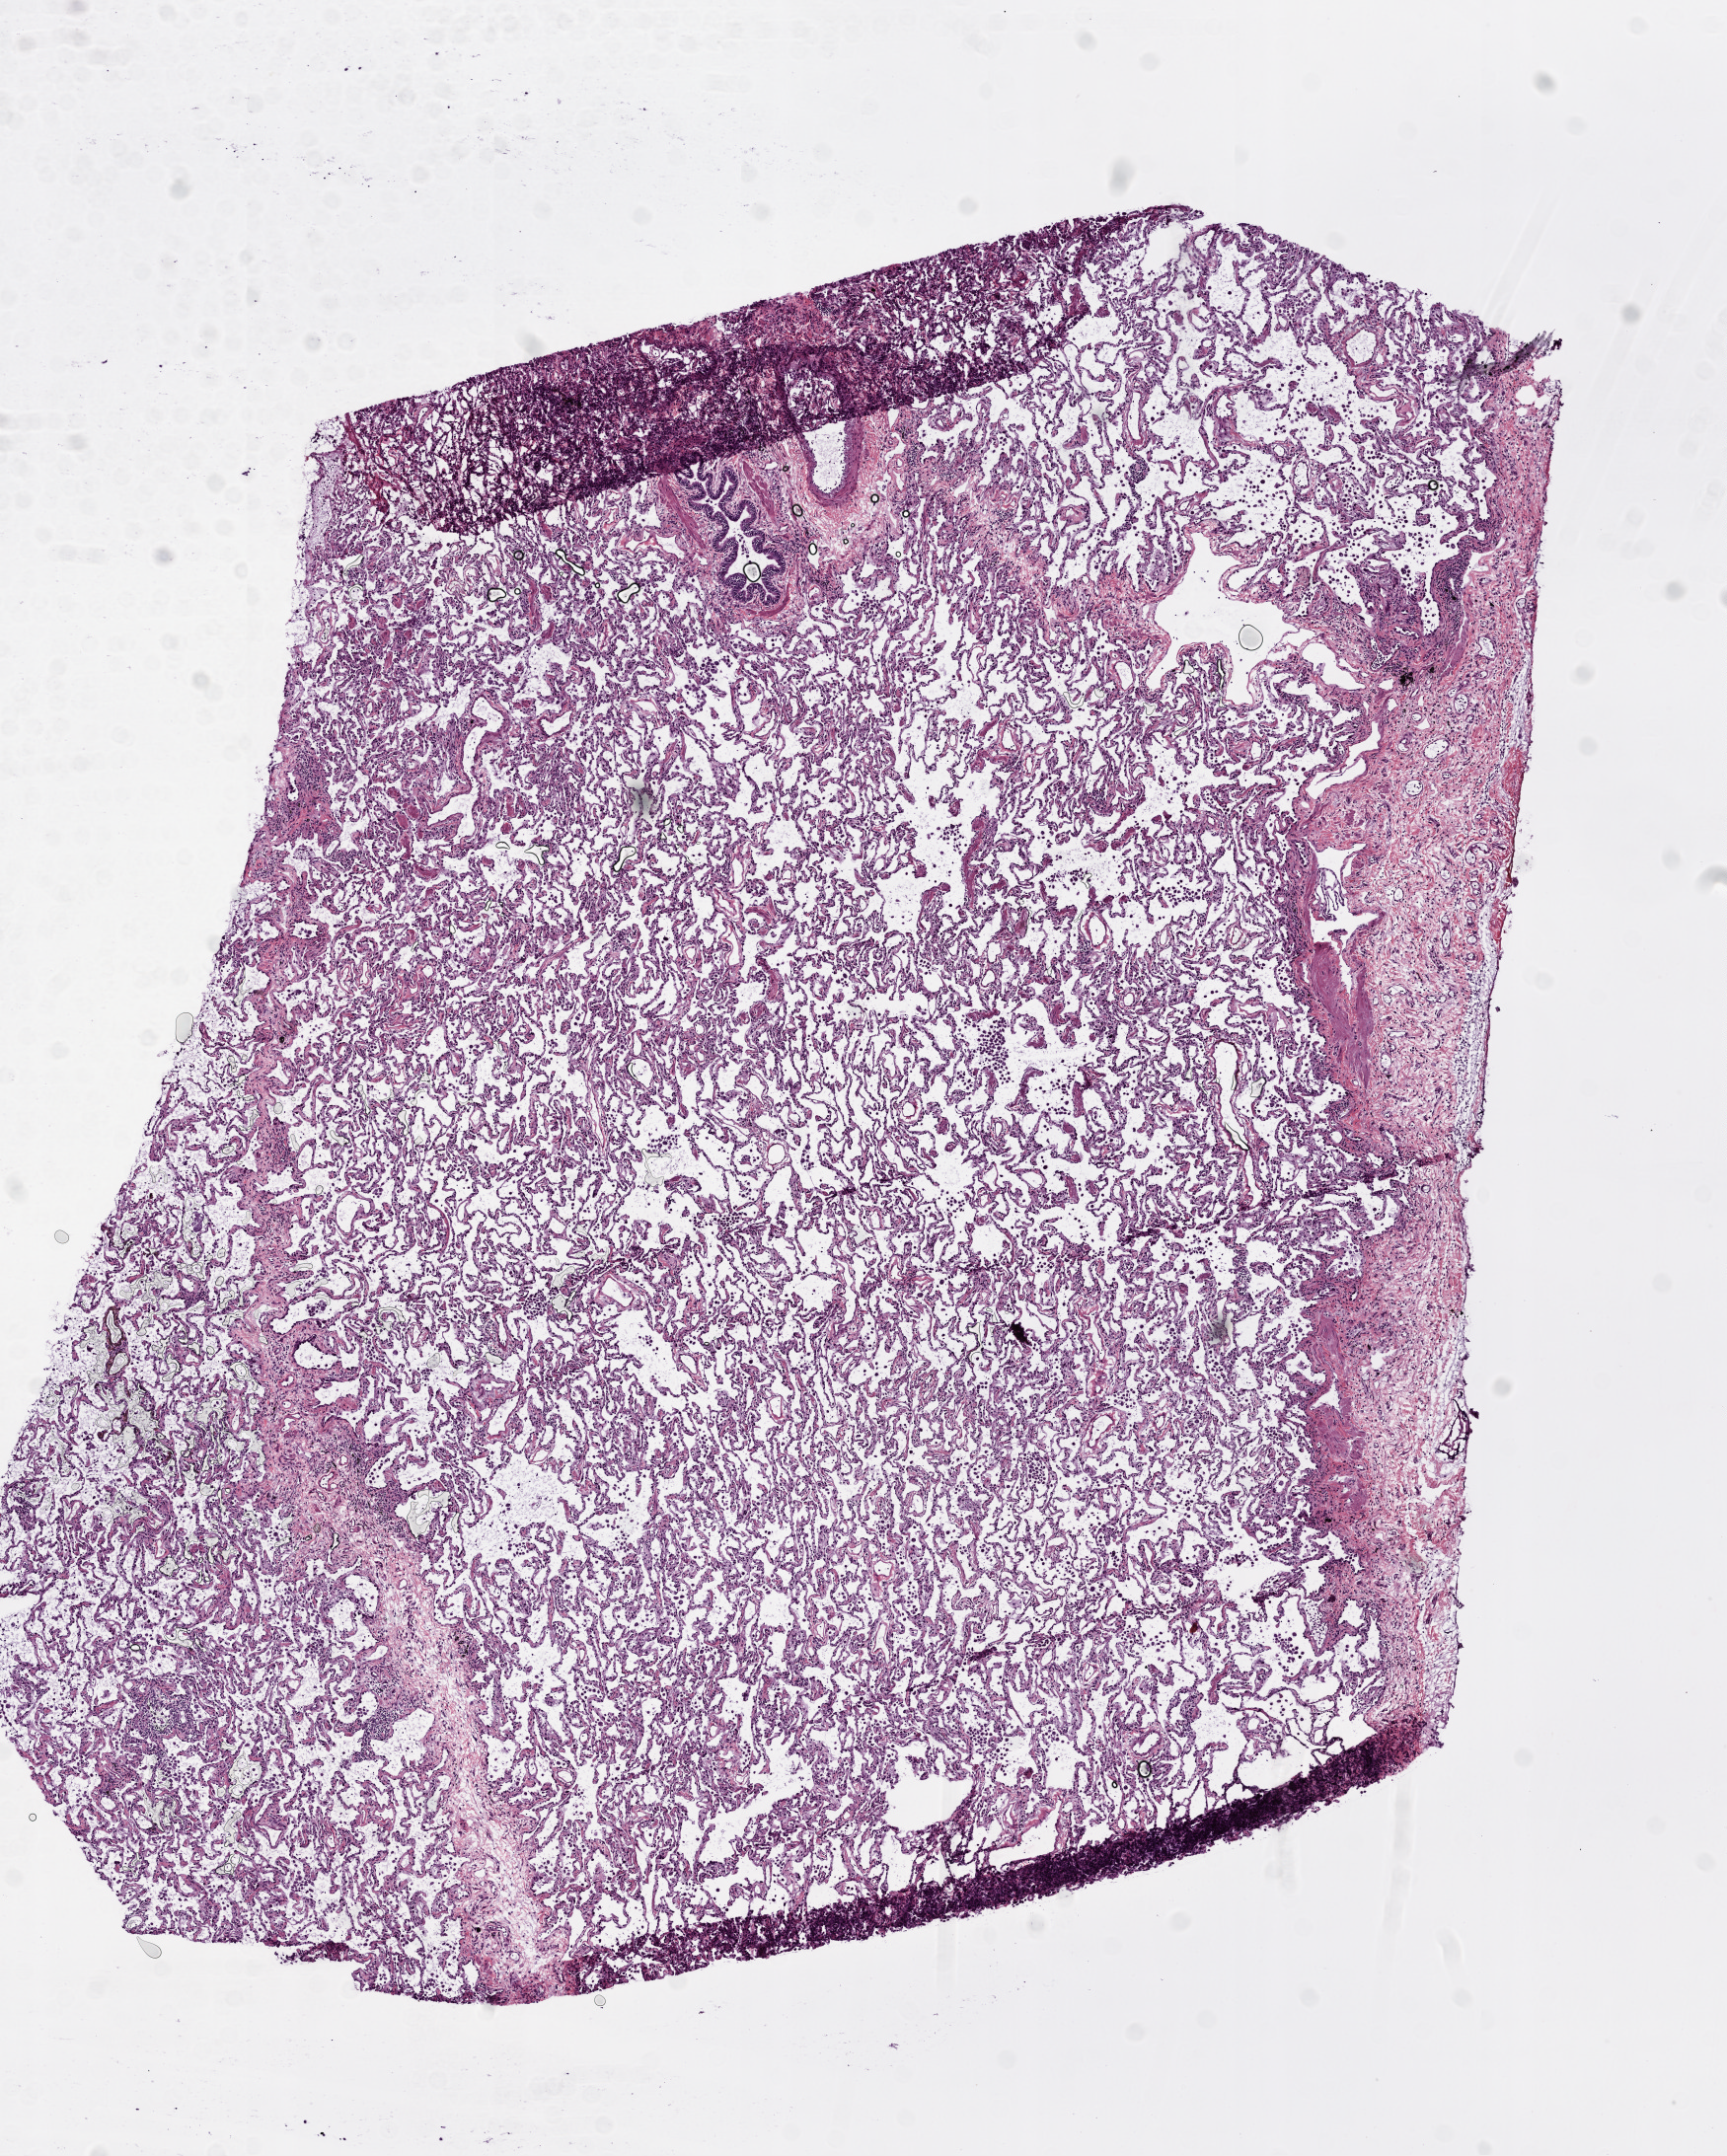
Whole-slide histology image, H&E-stained — low-resolution overview of the scanned area, about 7.0 x 8.8 mm (acquisition: 20x scan), frozen section from the top of the tissue portion, solid tissue normal (non-tumour tissue) sample from the lung. Patient: female, age at initial diagnosis 80 years.
• this section: solid tissue normal (non-tumour) sample from the same patient
• patient diagnosis: Adenocarcinoma, NOS (lower lobe, lung)